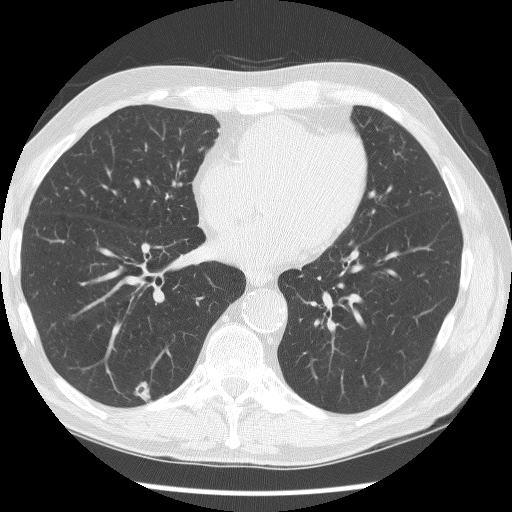
Axial slice from a low-dose chest CT screening exam; first (baseline) screen; lung window (W 1500 / L -600 HU); 2.5 mm slice thickness; lung (sharp) reconstruction kernel (BONE); slice 106 of 190 in the series. Male participant, aged 62 years at enrolment.
- Expert reader's lesion annotation, bounding box (x1, y1, x2, y2) in pixels: (126, 378, 165, 412).
- The screening reader recorded 2 non-calcified nodules or masses ≥4 mm on this exam; which of them this box marks is not recorded.
- Later outcome: lung cancer diagnosed 849 days after this screen — adenocarcinoma, NOS, right lower lobe, moderately differentiated (G2), stage IIIB (AJCC 6th edition), 15 mm at pathology.